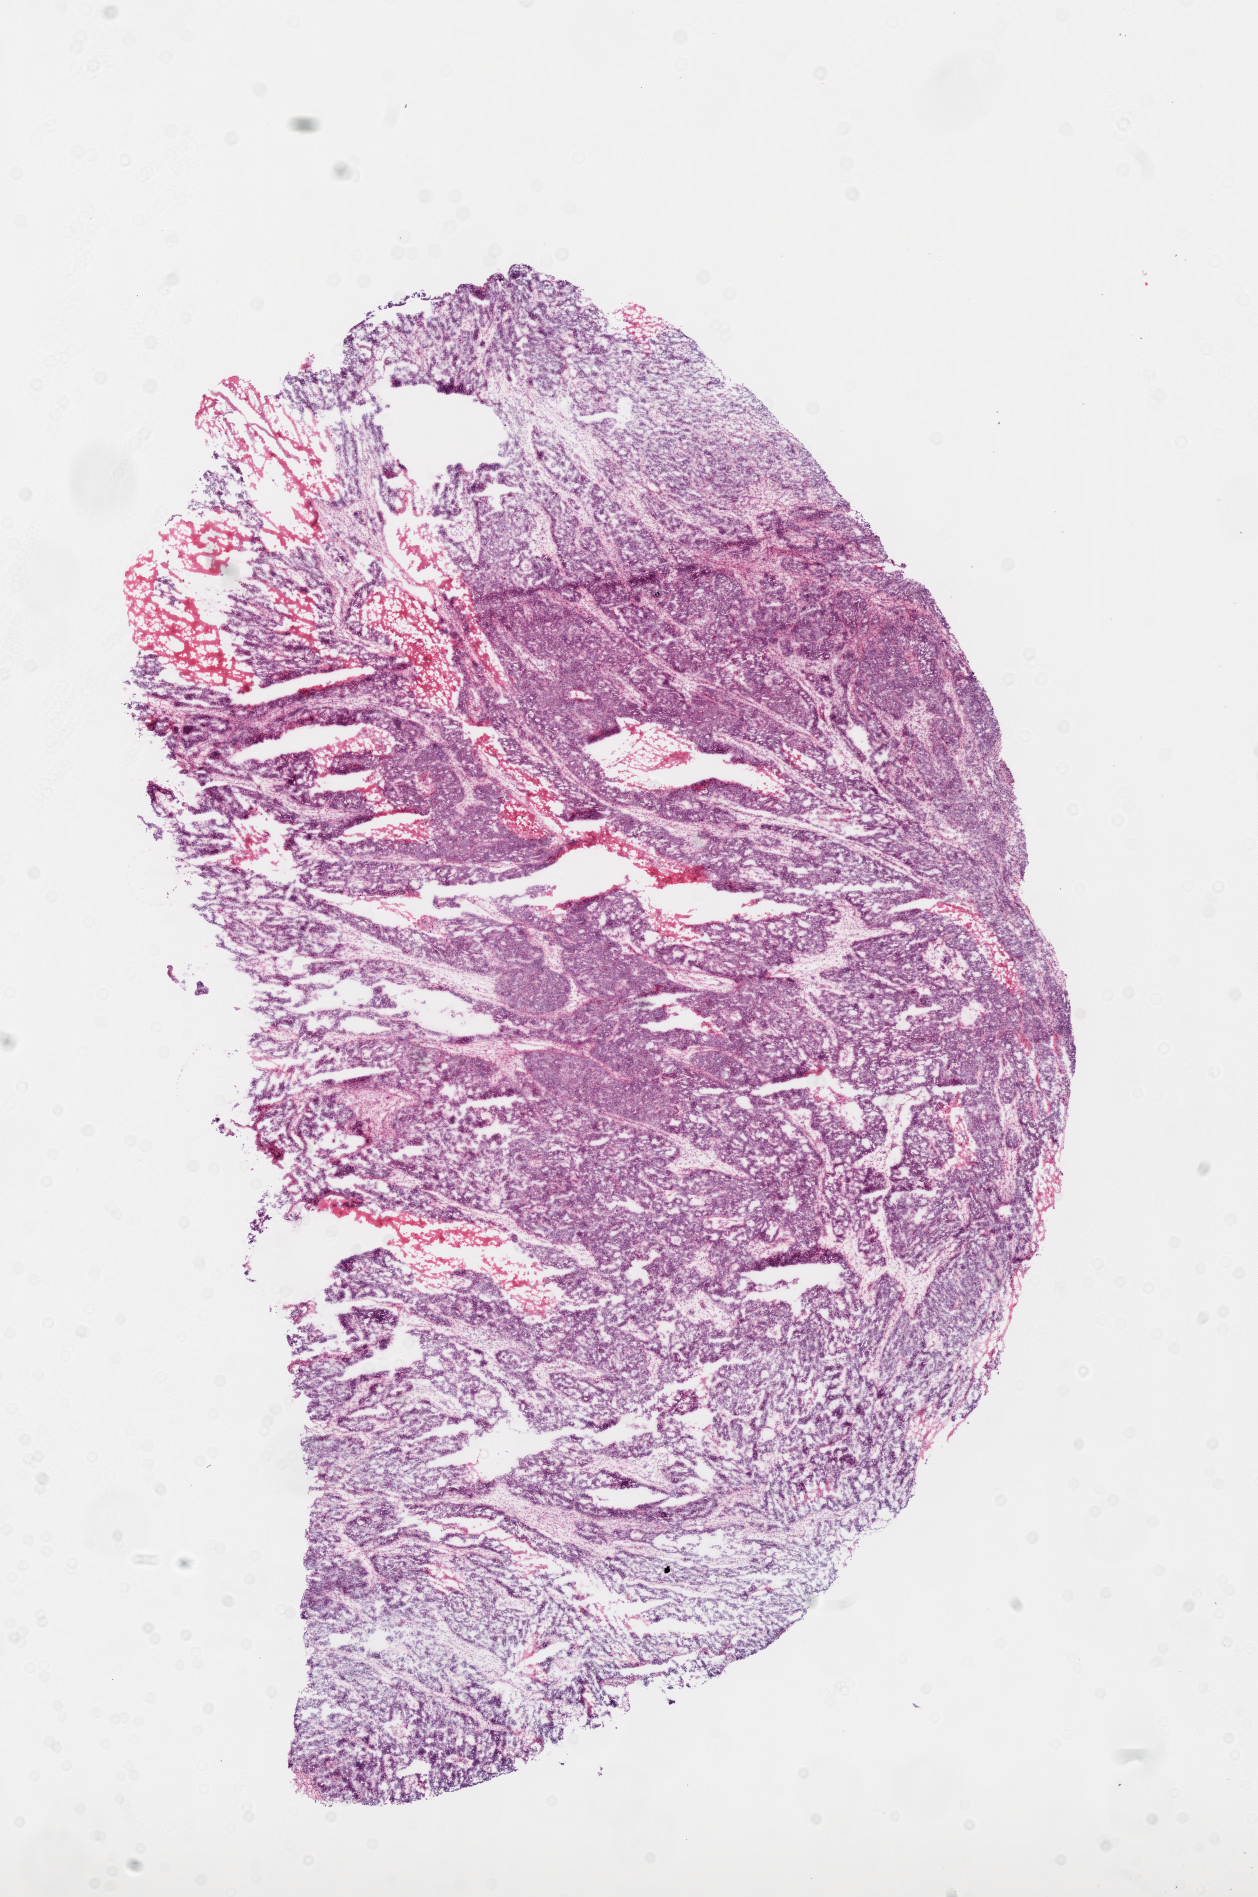
Hematoxylin and eosin (H&E) stained whole-slide image — whole scanned area (about 10.1 x 15.3 mm) shown as a low-resolution overview; frozen section; ovary, primary tumour sample. Patient: female, age at initial diagnosis 40 years. Histologic grade: G3 (poorly differentiated). Pathologist review of this section (percent, as recorded): tumour cells 85%, tumour nuclei 90%, normal cells 0%, stromal cells 15%, necrosis 0%.
- FIGO stage: IIIC
- laterality: bilateral
- pathologic diagnosis: Serous cystadenocarcinoma, NOS